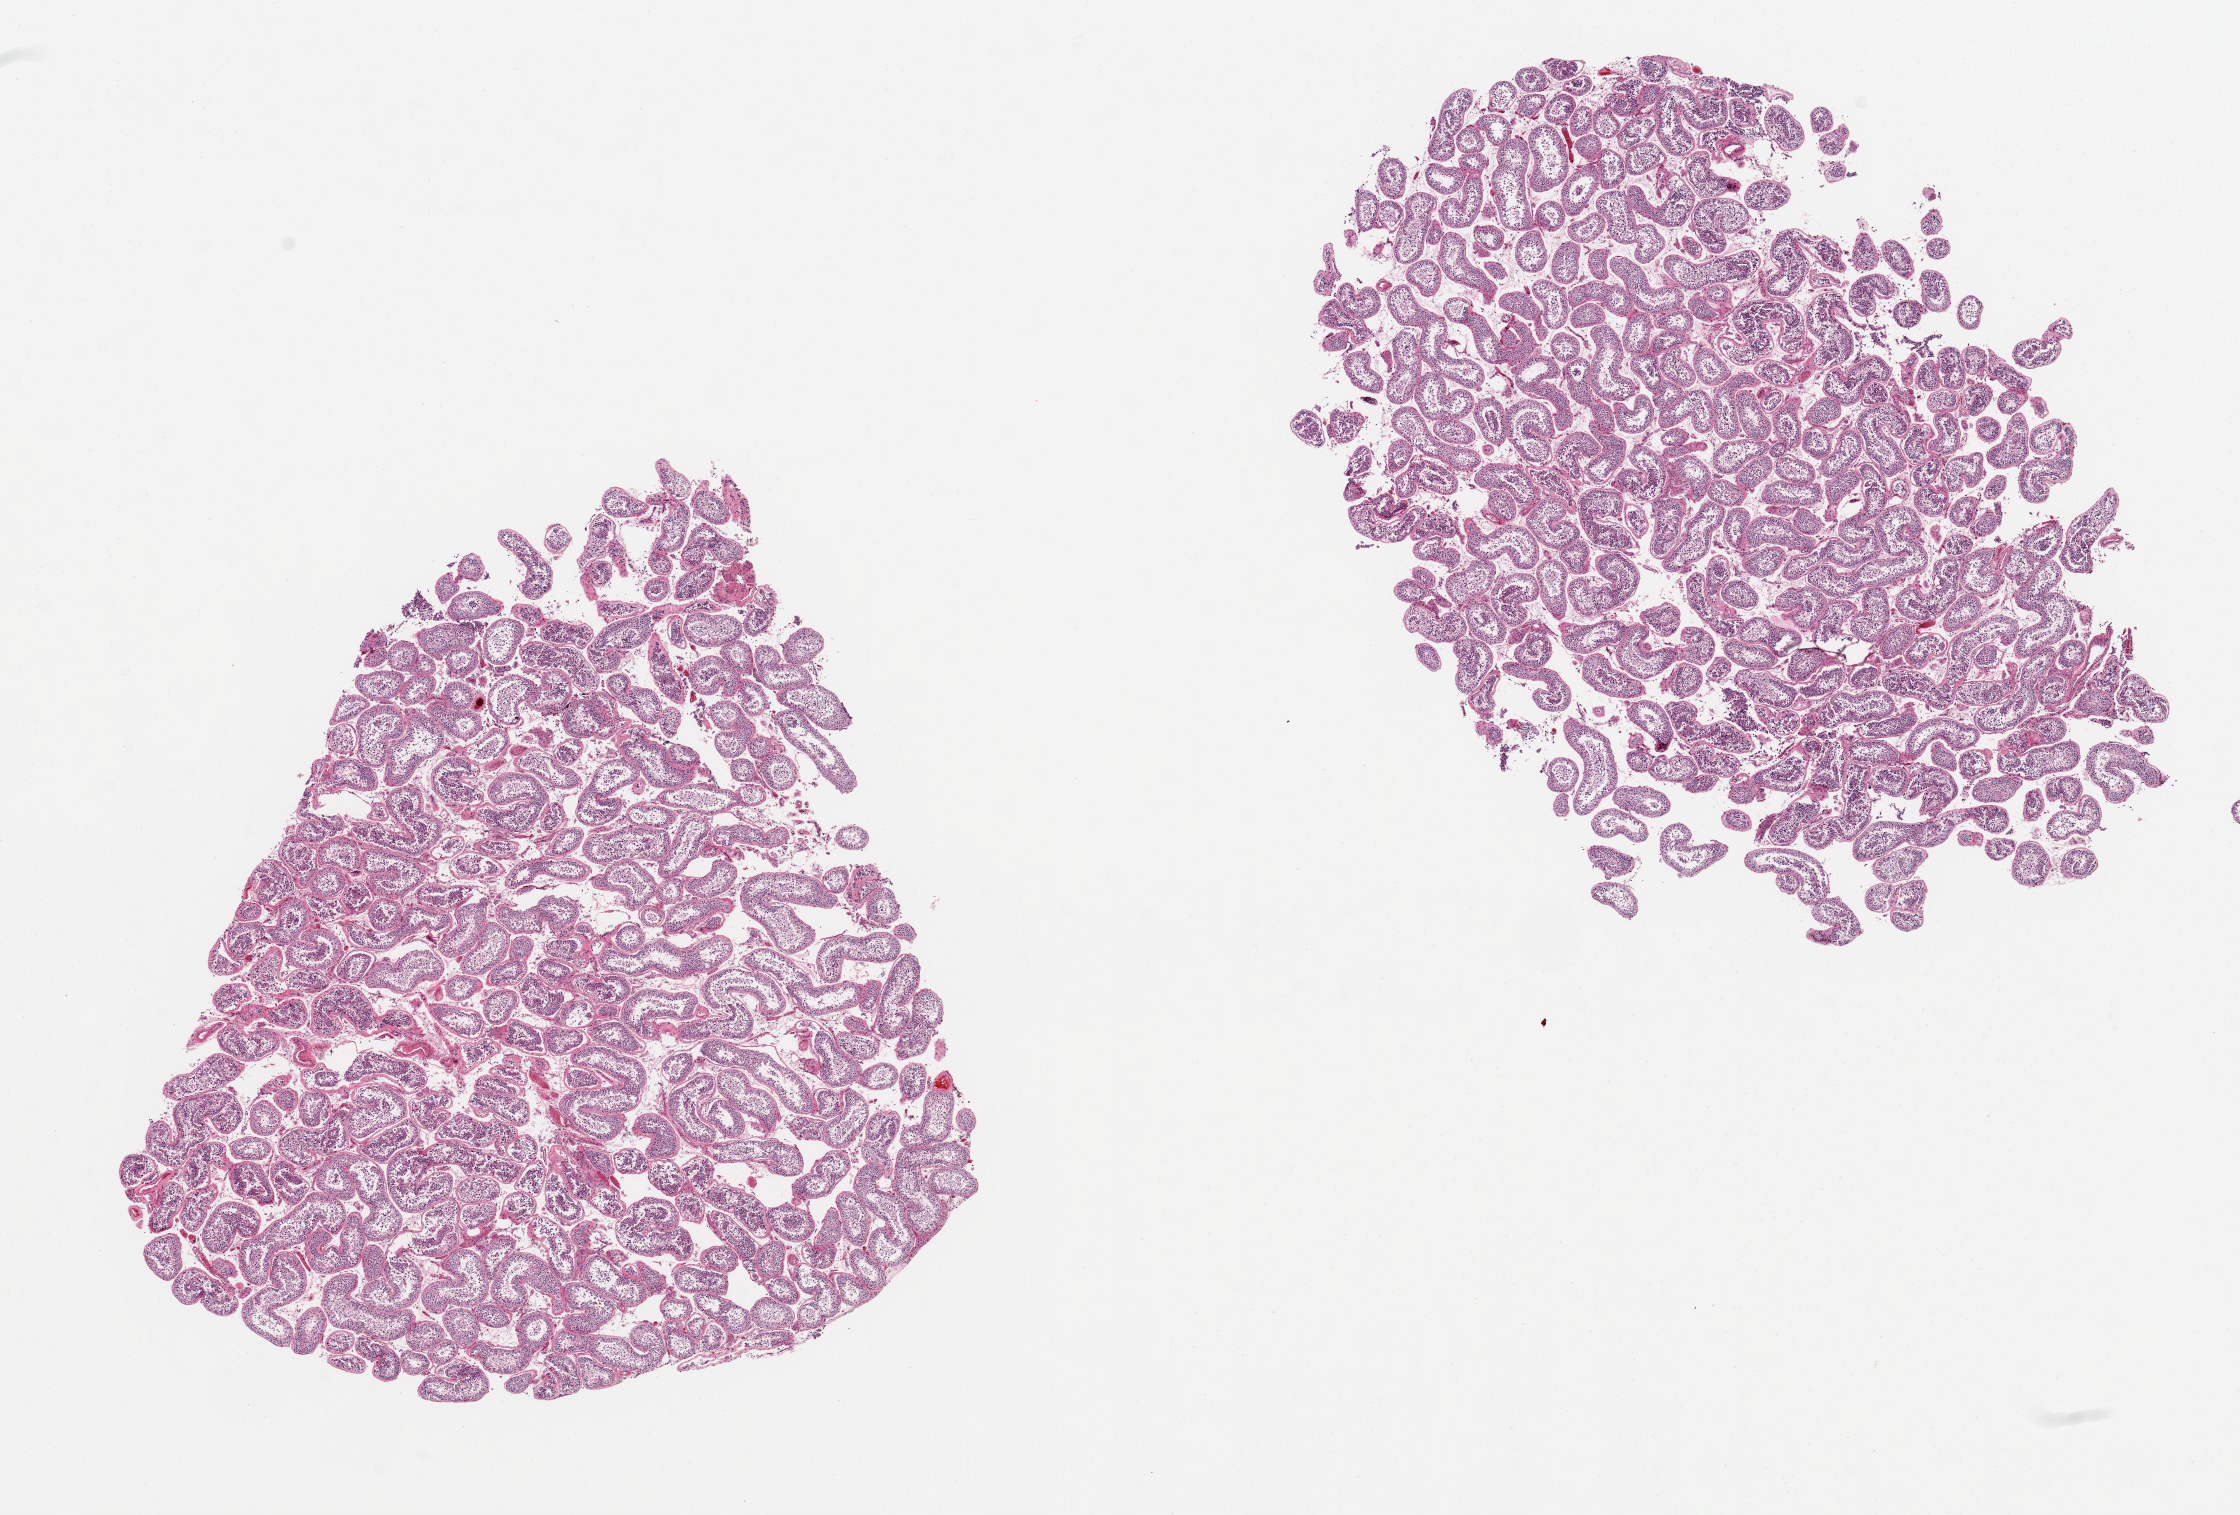
Digitized hematoxylin and eosin (H&E)-stained section, shown as a low-resolution overview of the whole scanned area (about 17.7 x 12.0 mm, slide scanned at 20x); PAXgene-fixed paraffin-embedded (PFPE) section; target tissue: testis; donor tissue sample. Donor: male.
Review note (as recorded): 2 pieces, 8x5 & 7x7 mm; spermatogenesis.